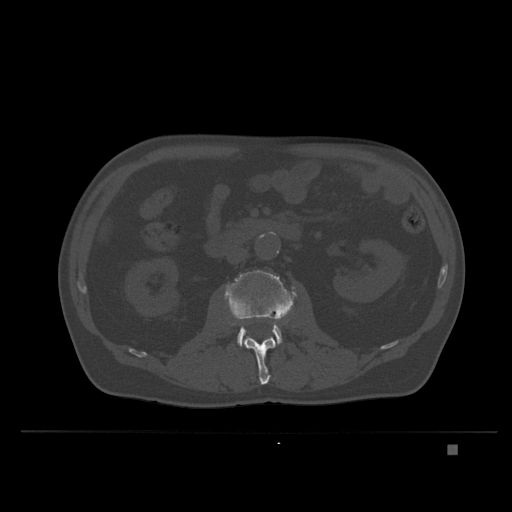
CT including the spine, one axial slice; slice 108 of 435 in the series (ordered by position); bone window (W 1800 / L 400 HU); 512 × 512 image matrix. Male patient, age 73 years. Case-level facts recorded for this patient, not image findings: primary cancer: skin.
Annotated regions visible in this slice (semi-automatically segmented with operator editing):
- L2 vertebra: box from (x=228, y=320) to (x=288, y=385) px
- L3 vertebra: (x=225, y=270)–(x=297, y=346)